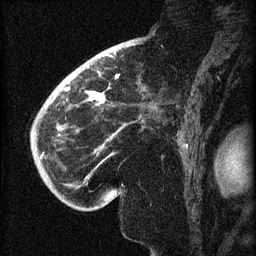
Breast MRI (dynamic contrast-enhanced), one sagittal slice; position 48 of 60 along the scan axis; dynamic contrast-enhanced series, image 2 of 3 at this slice position (ordered by acquisition); 1.5 T; TE 4.2 ms, TR 8.2 ms; 2 mm slice thickness; 256 × 256 image matrix. Patient: female, 71 years.
Structures marked on this image (semi-automatically segmented with operator editing):
- analysis volume of interest (the breast-tissue region the enhancement analysis was run in; not a lesion): box from (x=40, y=72) to (x=145, y=196) px
- tumour enhancement mask (voxels above the 70 % enhancement threshold inside the analysis volume of interest): (x=41, y=87)–(x=105, y=157)